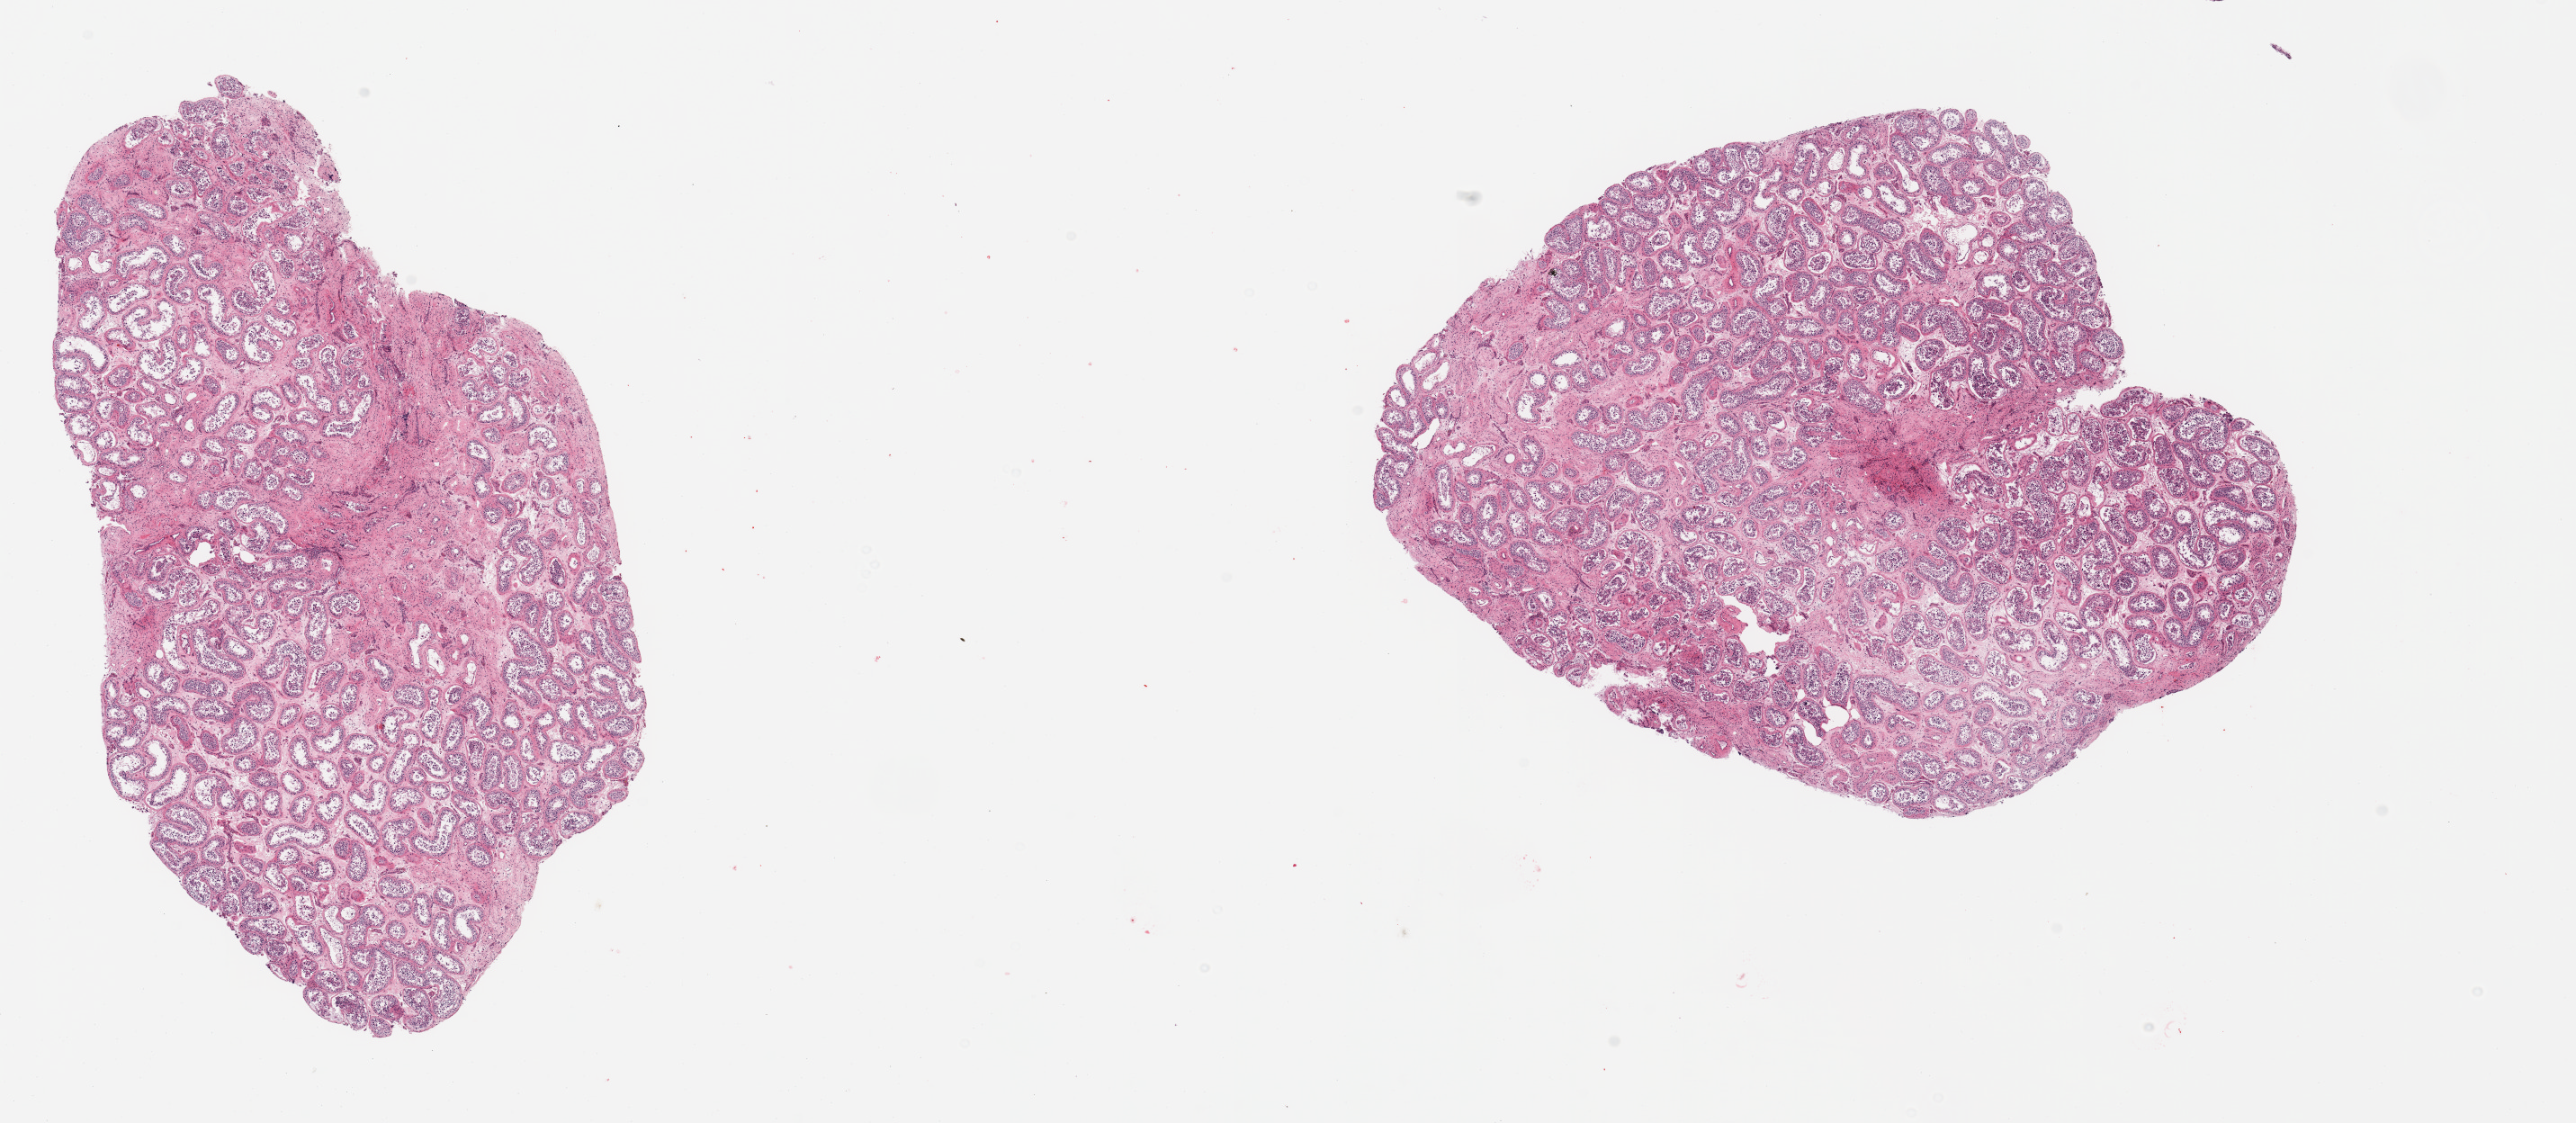
Digitized haematoxylin and eosin-stained section, a low-resolution overview of the entire scanned area, about 22.6 x 9.9 mm; PAXgene-fixed, paraffin-embedded tissue; sampled site (target tissue): testis; donor tissue sample. Donor sex: male.
Reviewer comment on this tissue sample: 2 pieces; foci of fibrosis up to 3 sq mm.